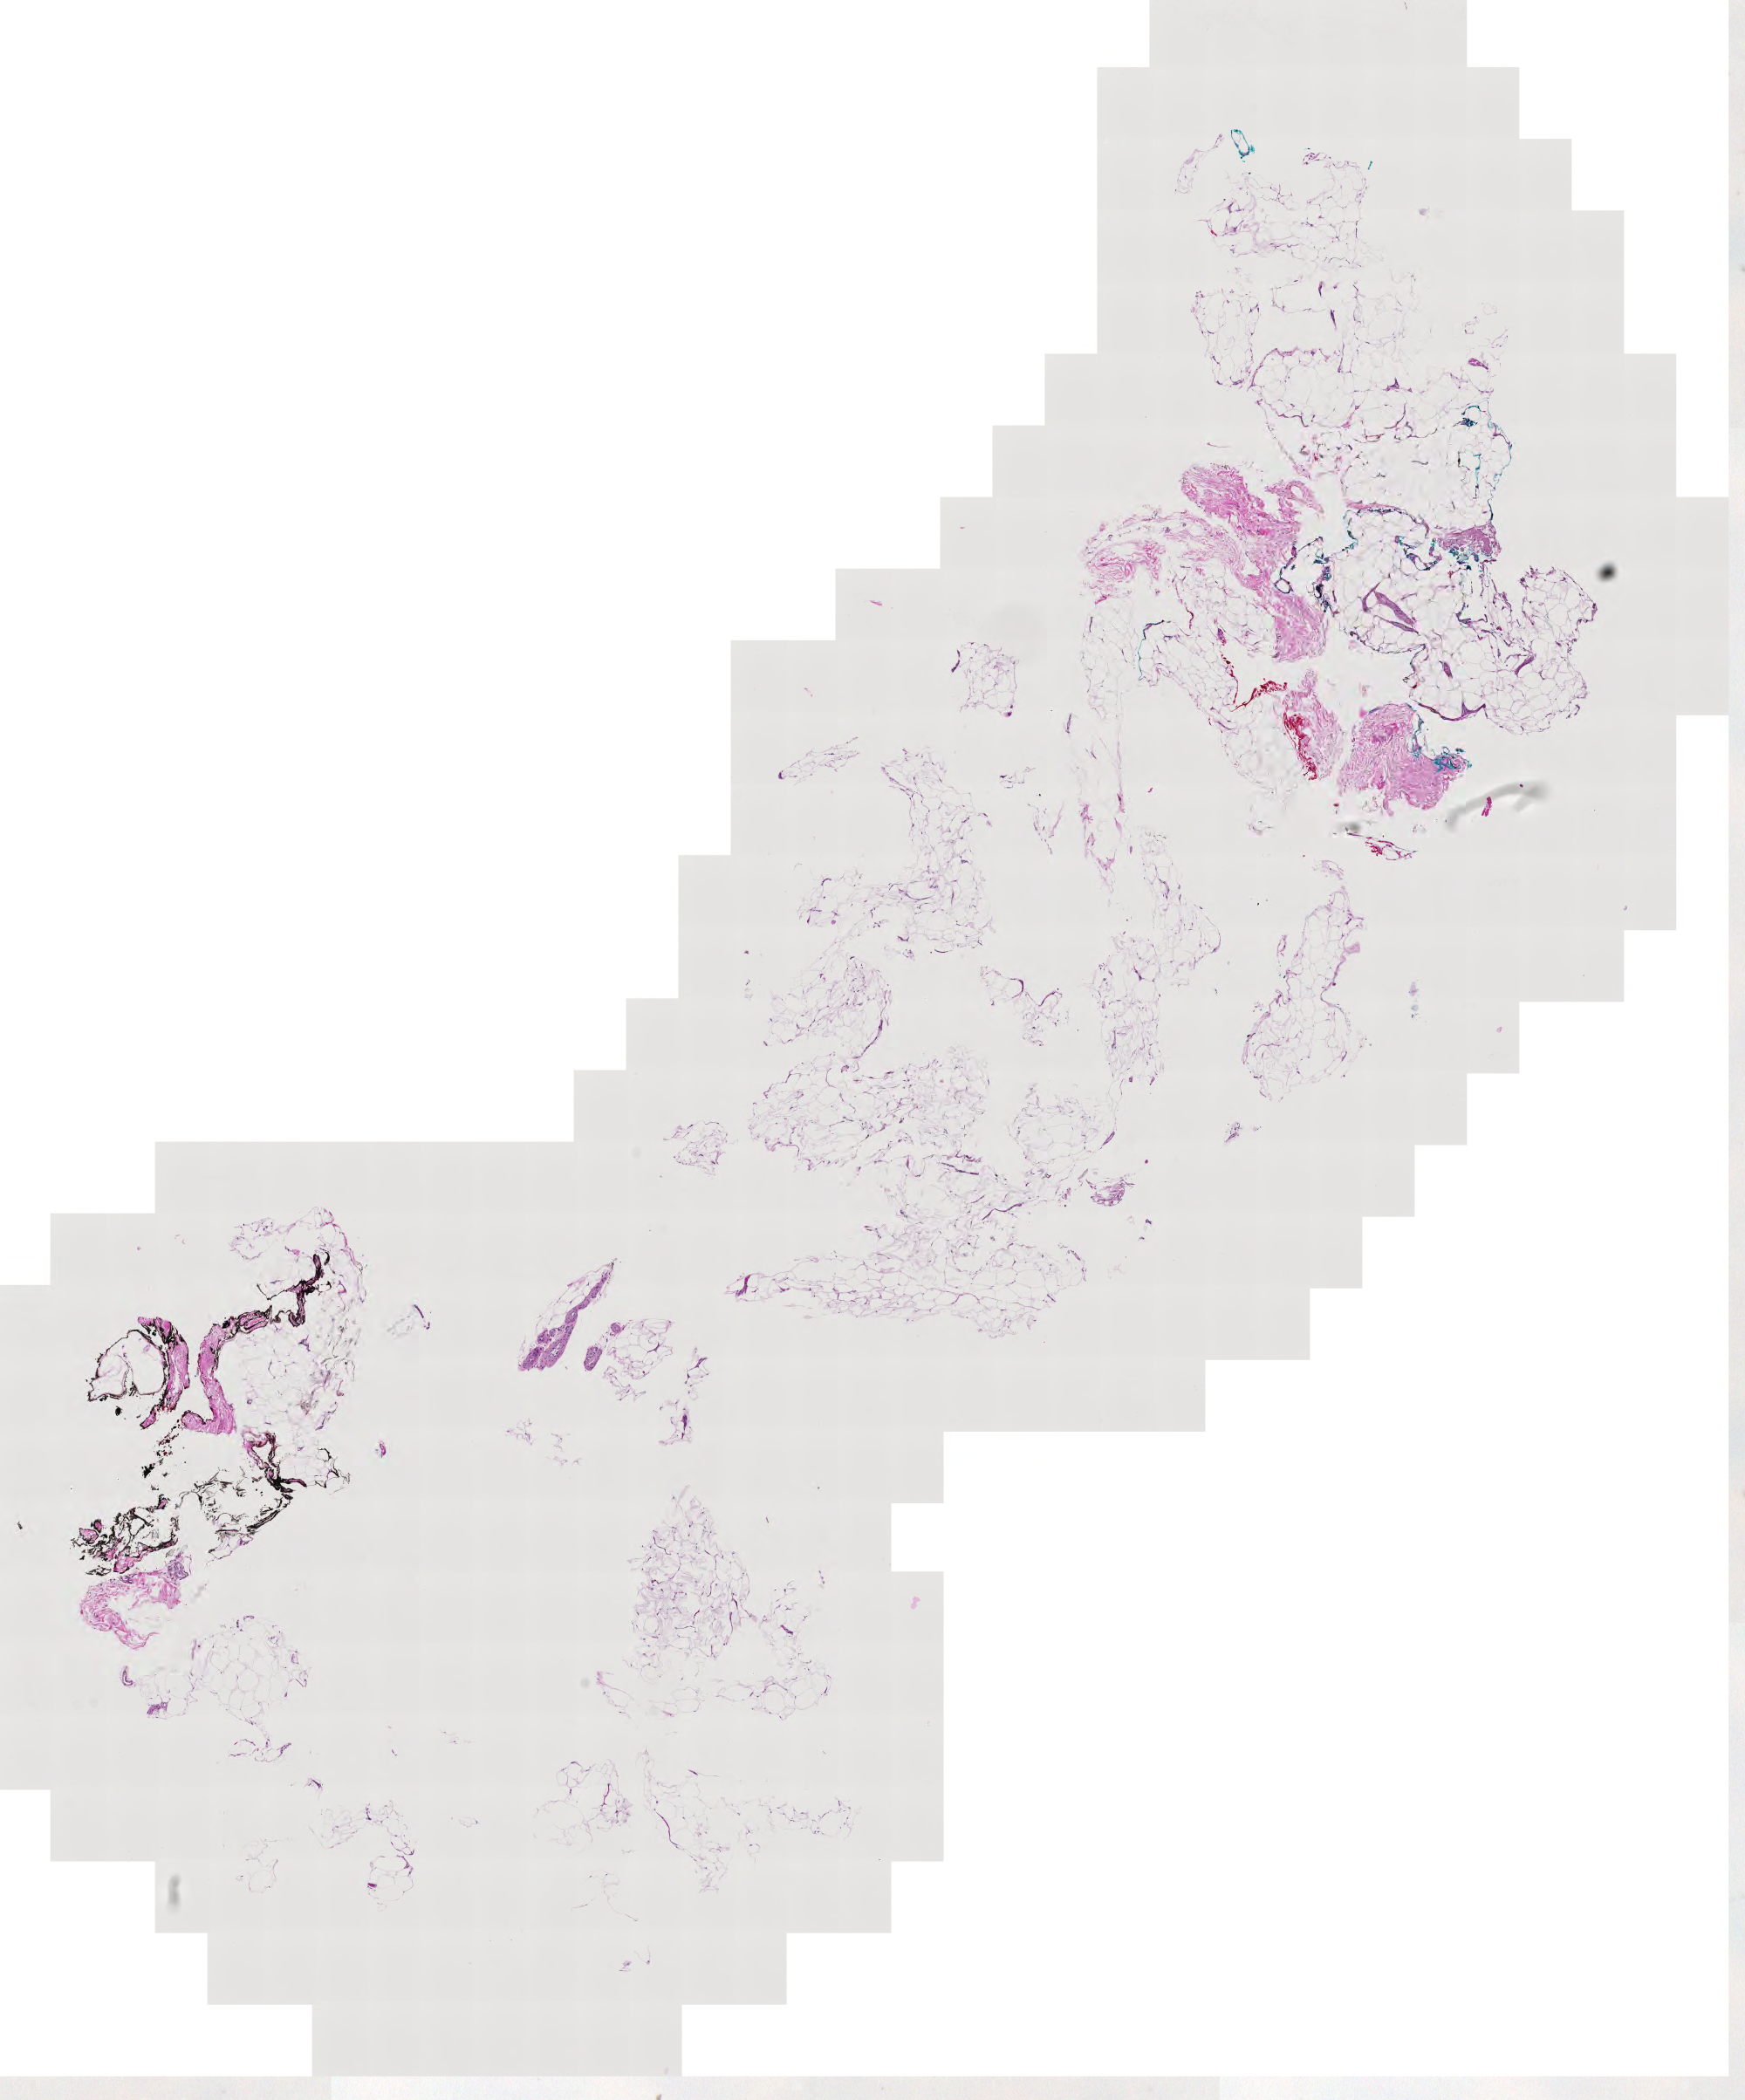
Digitized H&E tissue section (whole slide), low-resolution overview of the scanned area, about 10.3 x 12.4 mm (slide scanned at 20x); normal (non-tumour) tissue sample. 74-year-old male patient.
* this section: normal (non-tumour) tissue from the same patient
* patient diagnosis (cohort enrolment): sarcoma (site not recorded at cohort level)